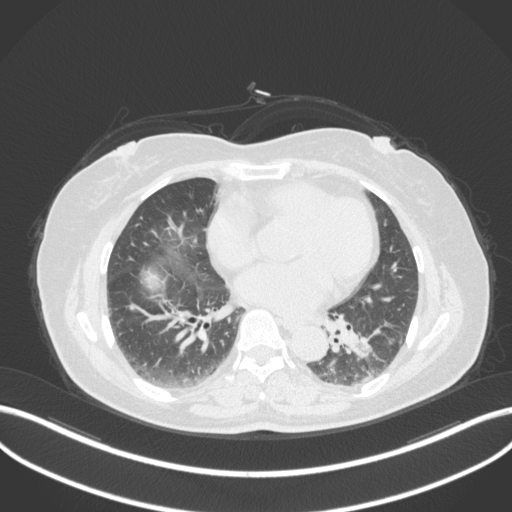
Chest CT, one axial slice; slice 161 of 307 in the series (ordered by position); lung window (W 1500 / L -600 HU); 1 mm slice thickness; 512 × 512 image matrix, field of view 400 × 400 mm. Patient: female, 59 years. Case-level facts recorded for this patient, not image findings: clinical TNM (as recorded): T2a N0 M0.
Outlined on this slice (rectangle marked by the reading radiologist):
- lung tumour (recorded histology: adenocarcinoma): bounding box <348,325,383,361> (left, top, right, bottom; pixels)